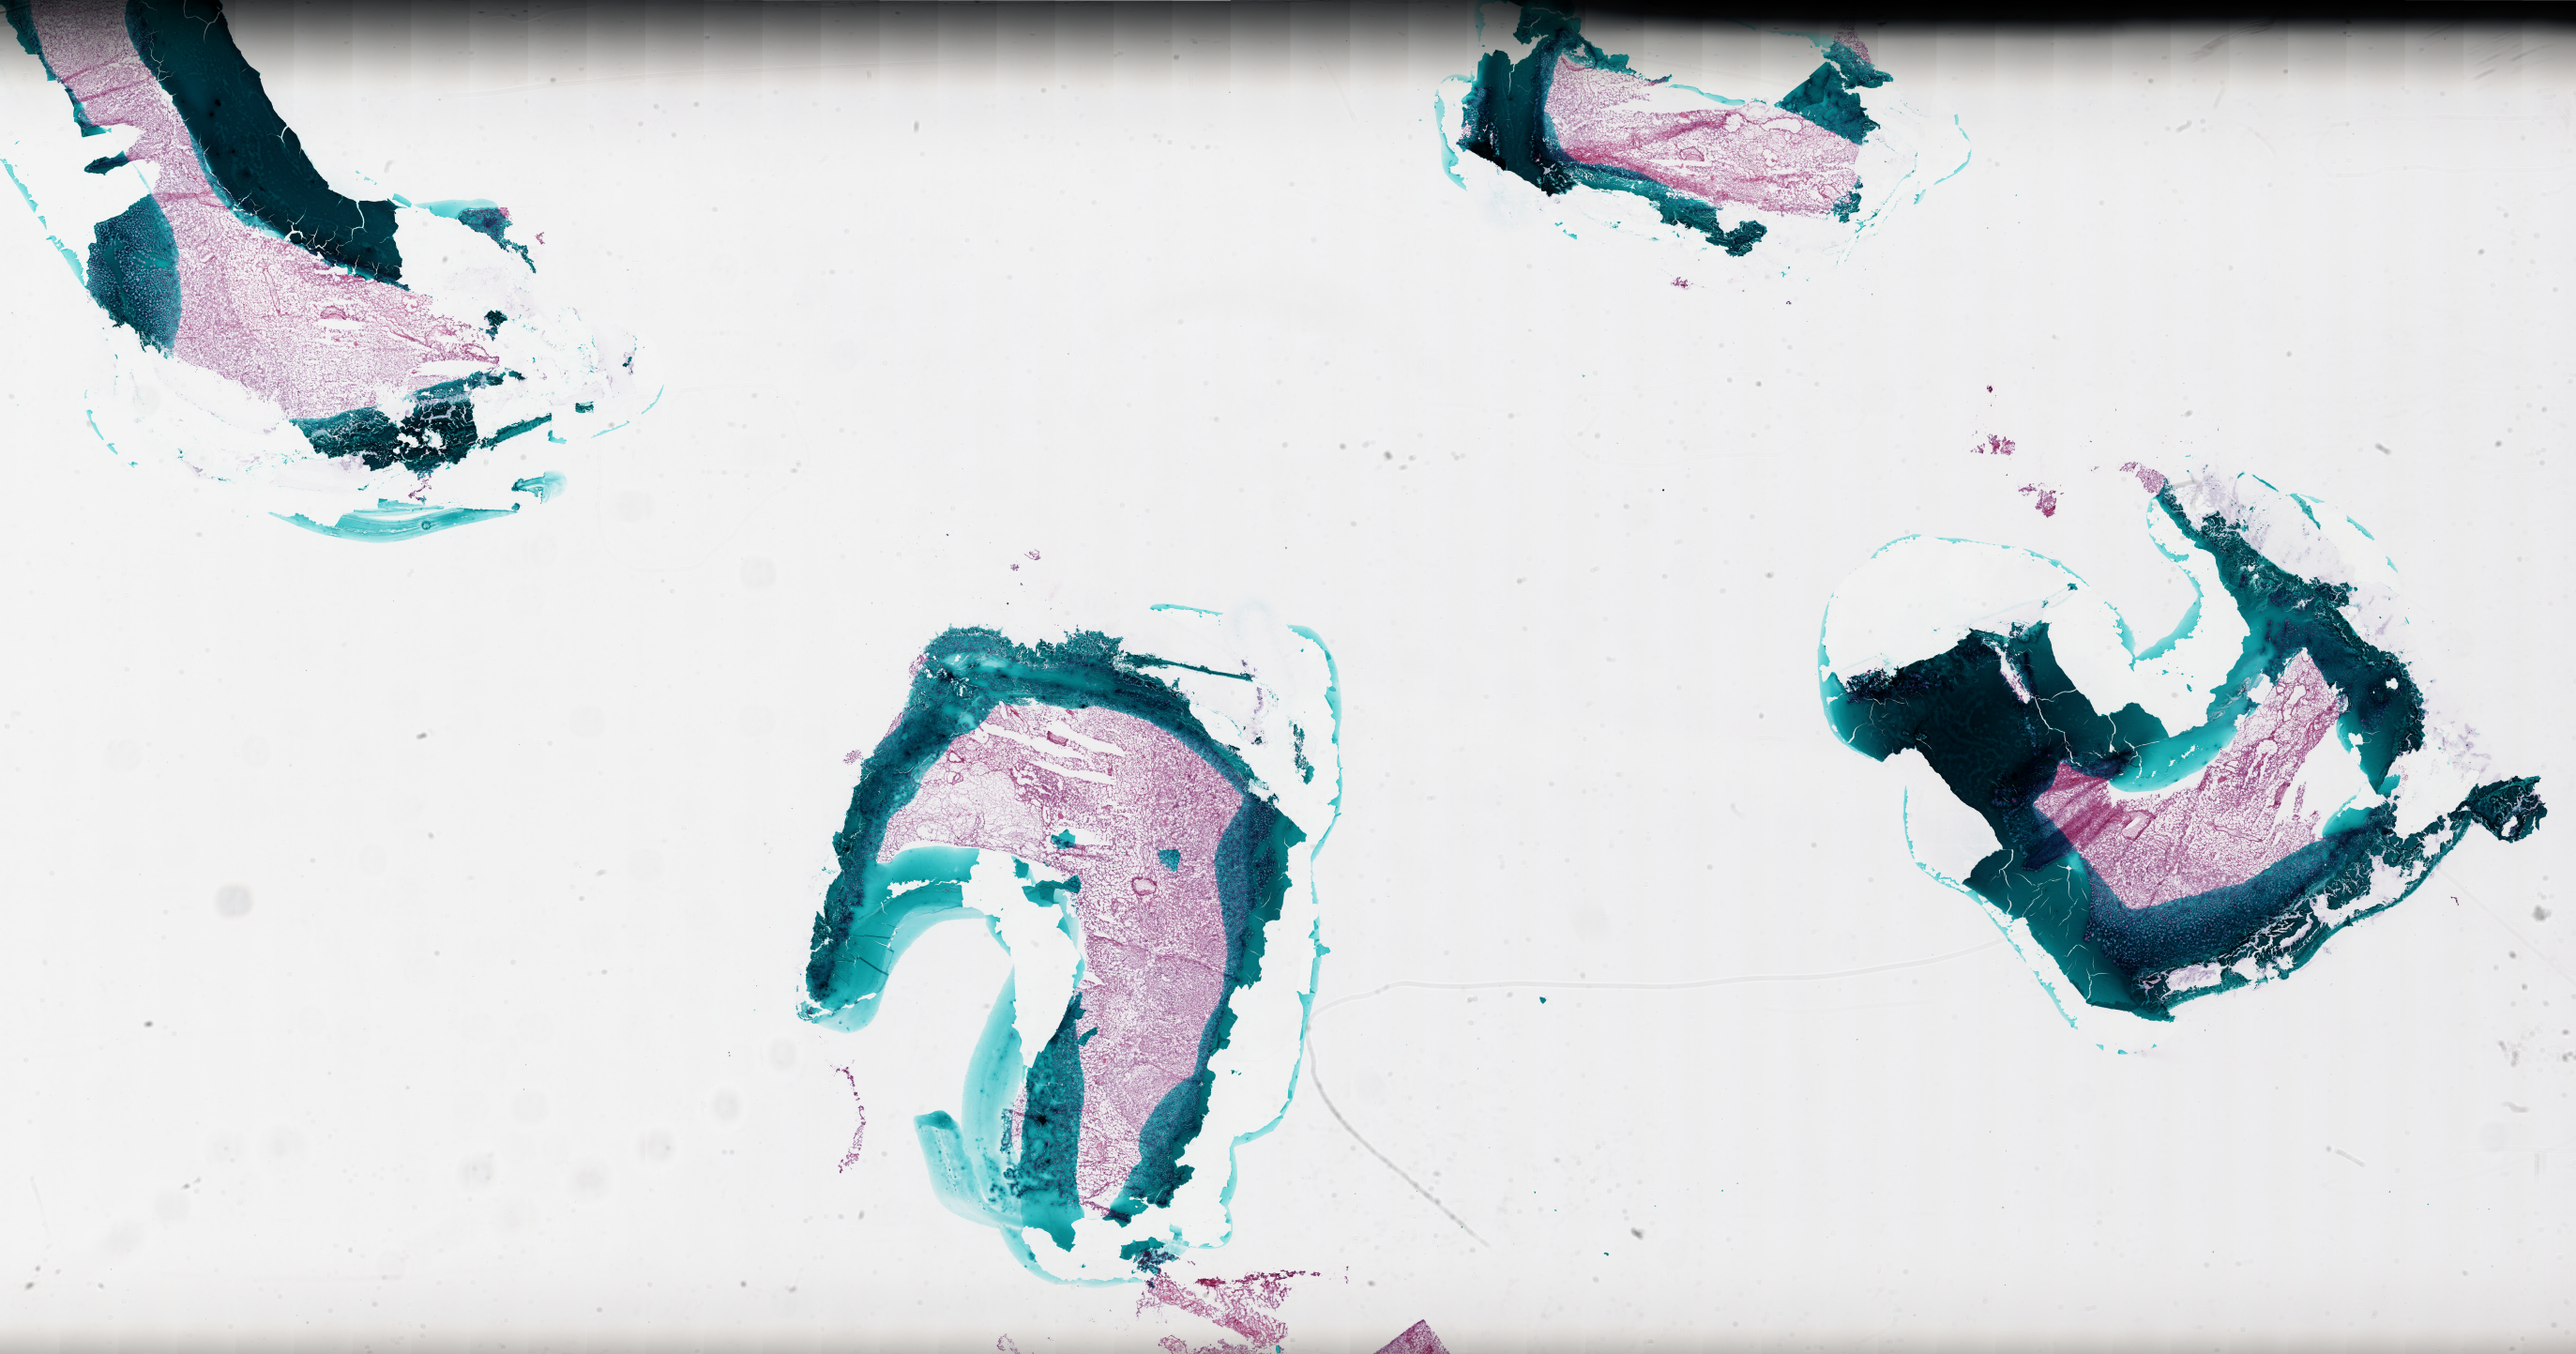
Hematoxylin and eosin (H&E) stained whole-slide image — a low-resolution overview of the entire scanned area, about 44.0 x 23.1 mm. Frozen section from the bottom of the tissue portion. Primary tumour sample from the brain. Male patient; age at initial diagnosis 60 years. Pathologist review of this section (percent, as recorded): tumour cells 80%, tumour nuclei 100%, normal cells 0%, stromal cells 0%, necrosis 20%.
Pathologic diagnosis: Glioblastoma.